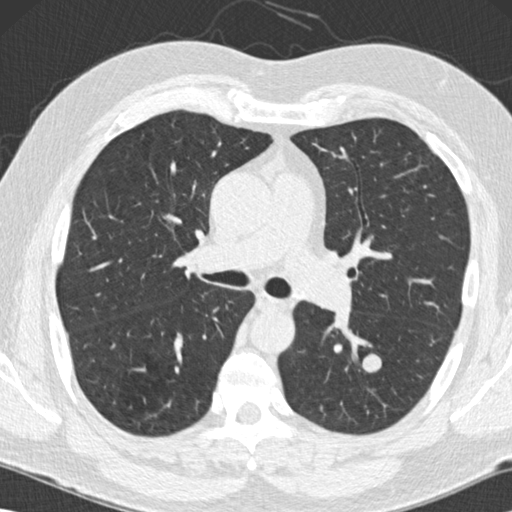
Low-dose screening chest CT, one axial slice. Position 88 of 152 along the scan axis. Reconstruction kernel B30f. Lung window (W 1500 / L -600 HU). 2 mm slice thickness. 512 × 512 image matrix.
Structures marked on this image (expert manual segmentation):
- lesion 2 (nodule, lower lobe of left lung): bounding box [x1, y1, x2, y2] px = [362, 354, 382, 373]